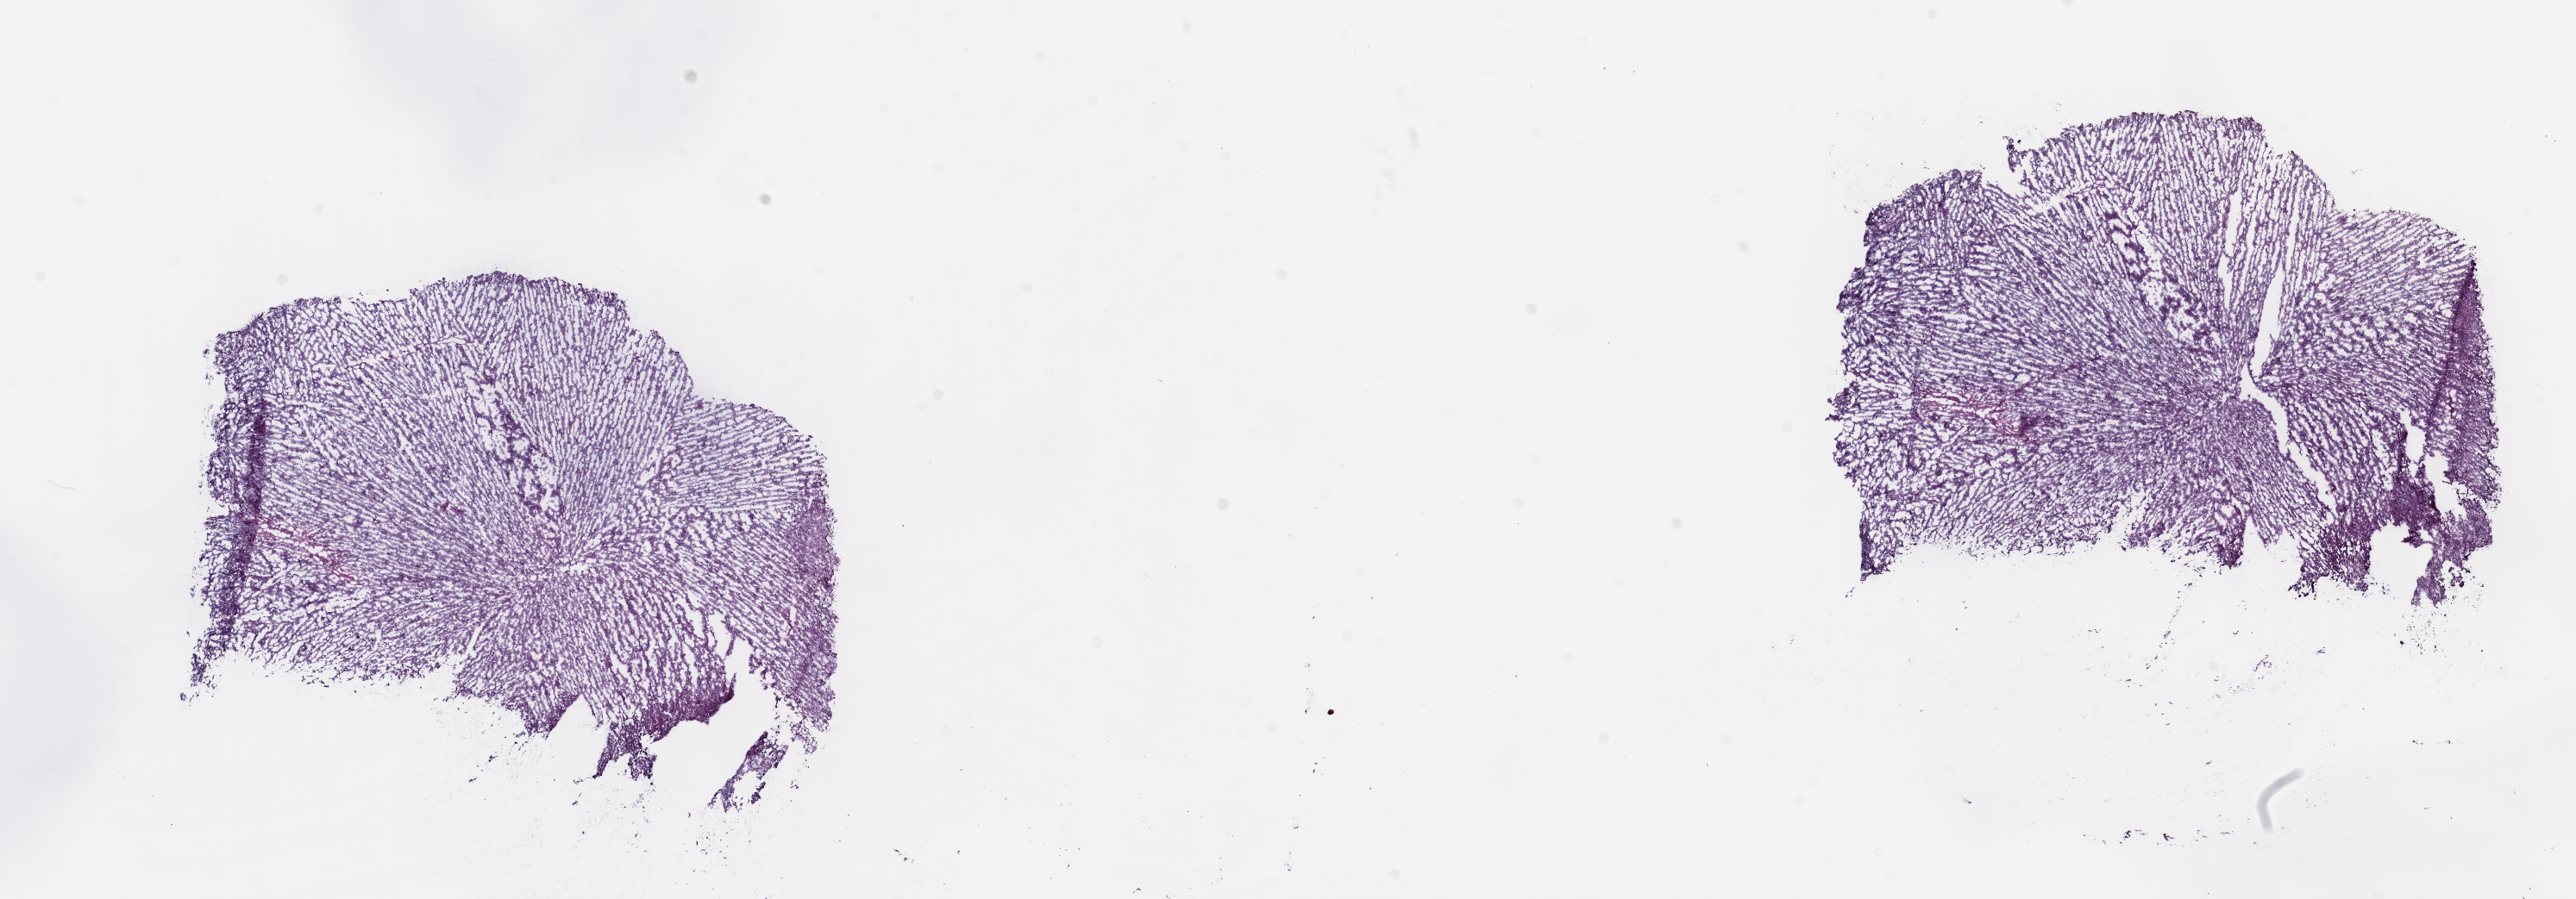
Digitized H&E tissue section (whole slide), whole scanned area (about 24.2 x 8.4 mm) shown as a low-resolution overview; frozen section from the top of the tissue portion; brain, primary tumour sample. Patient: female, age at initial diagnosis 48 years. Histologic grade: G2 (moderately differentiated). Composition of this section per pathologist review: tumour cells 50%, tumour nuclei 85%, normal cells 10%, stromal cells 40%, necrosis 0%. Infiltration values recorded for this section: lymphocyte infiltration 0%, monocyte infiltration 0%, neutrophil infiltration 0%.
- diagnosis: Mixed glioma (cerebrum)
- laterality: left